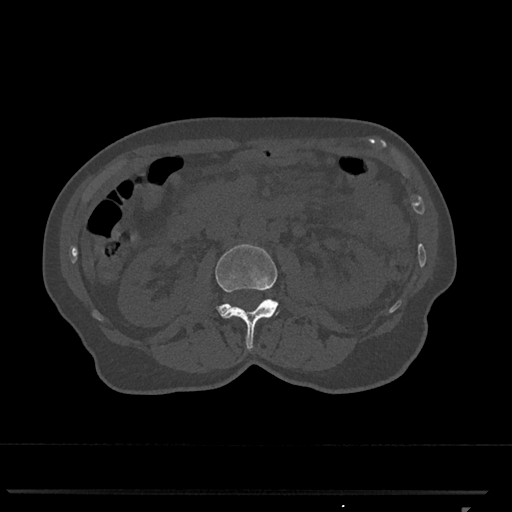
CT including the spine, one axial slice. Slice 331 of 793 in the series (ordered by position). Reconstruction kernel Br40s/3. 120 kVp. Bone window (W 1800 / L 400 HU). 0.5 mm slice thickness. 512 × 512 image matrix. Patient: female, 62 years. From the clinical record (not read from this slice): primary cancer: renal.
Structures marked on this image (semi-automatic segmentation, software-assisted and operator-edited):
- L2 vertebra: box from (x=215, y=244) to (x=279, y=351) px